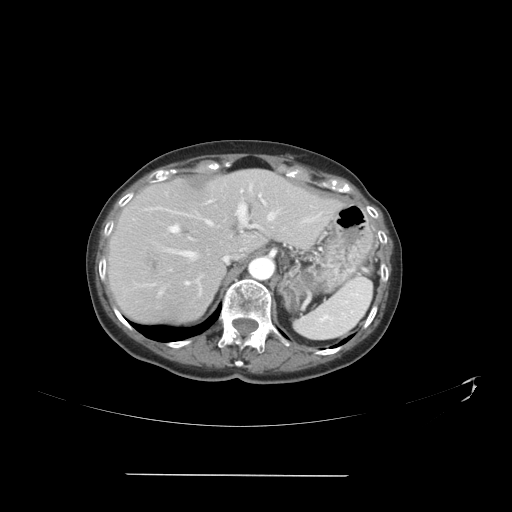
Contrast-enhanced abdominal CT, one axial slice; slice 28 of 41 in the series (ordered by position); 120 kVp; intravenous contrast given; soft-tissue window (W 400 / L 40 HU); 512 × 512 image matrix, field of view 431 × 431 mm. Female patient, age 74 years. From the clinical record (not read from this slice): diagnosis: colorectal cancer liver metastases, imaged before liver resection.
Outlined on this slice (expert manual segmentation):
- hepatic veins: box from (x=143, y=192) to (x=275, y=293) px
- liver: (x=107, y=170)–(x=338, y=326)
- planned liver remnant (the part of the liver to remain after resection): (x=113, y=170)–(x=315, y=260)
- portal vein (with intrahepatic branches): (x=169, y=190)–(x=264, y=285)
- liver metastasis: (x=325, y=203)–(x=329, y=208)
- liver metastasis: (x=144, y=251)–(x=159, y=273)